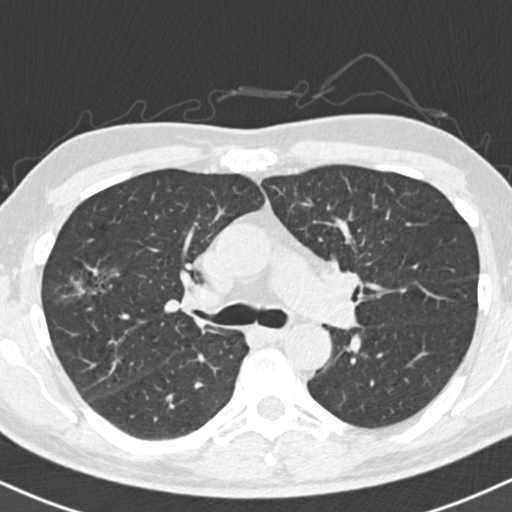
Axial slice from a low-dose chest CT screening exam, baseline screening round, lung window (W 1500 / L -600 HU), 2 mm slice thickness, standard (soft-tissue) reconstruction kernel (B30f), 120 kVp, slice 59 of 154 in the series. Male, age 56 years at enrolment. Former smoker at enrolment.
Lesion marked by an expert reader, bounding box (x1, y1, x2, y2) in pixels: (49, 254, 138, 318). Screening reader's record for this exam: no non-calcified nodule ≥4 mm recorded. Later outcome: lung cancer diagnosed 392 days after this screen (after the second annual screen) — bronchiolo-alveolar adenocarcinoma, NOS, right upper lobe, well differentiated (G1), stage IIB (AJCC 6th edition), 30 mm at pathology.